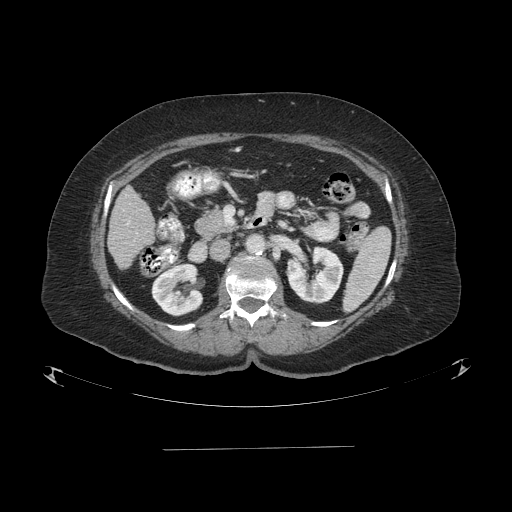
Contrast-enhanced abdominal CT (liver protocol), one axial slice. Reconstruction kernel STANDARD. 120 kVp. One of 2 acquisitions stored at this slice position. Soft-tissue window (W 400 / L 40 HU). 2.5 mm slice thickness. 512 × 512 image matrix, field of view 500 × 500 mm. From the clinical record (not read from this slice): diagnosis: hepatocellular carcinoma (patient treated with transarterial chemoembolisation; whether this scan precedes or follows treatment is not stated here); TNM stage (as recorded): Stage-IIIA; Child-Pugh class: A; tumour differentiation: poorly differentiated; tumour size: 5.2 cm.
Outlined on this slice (semi-automatic segmentation, software-assisted and operator-edited):
- liver parenchyma outside the tumour (the mass and vessels are separate outlines, so this box may not span the whole liver): box from (x=108, y=186) to (x=154, y=268) px